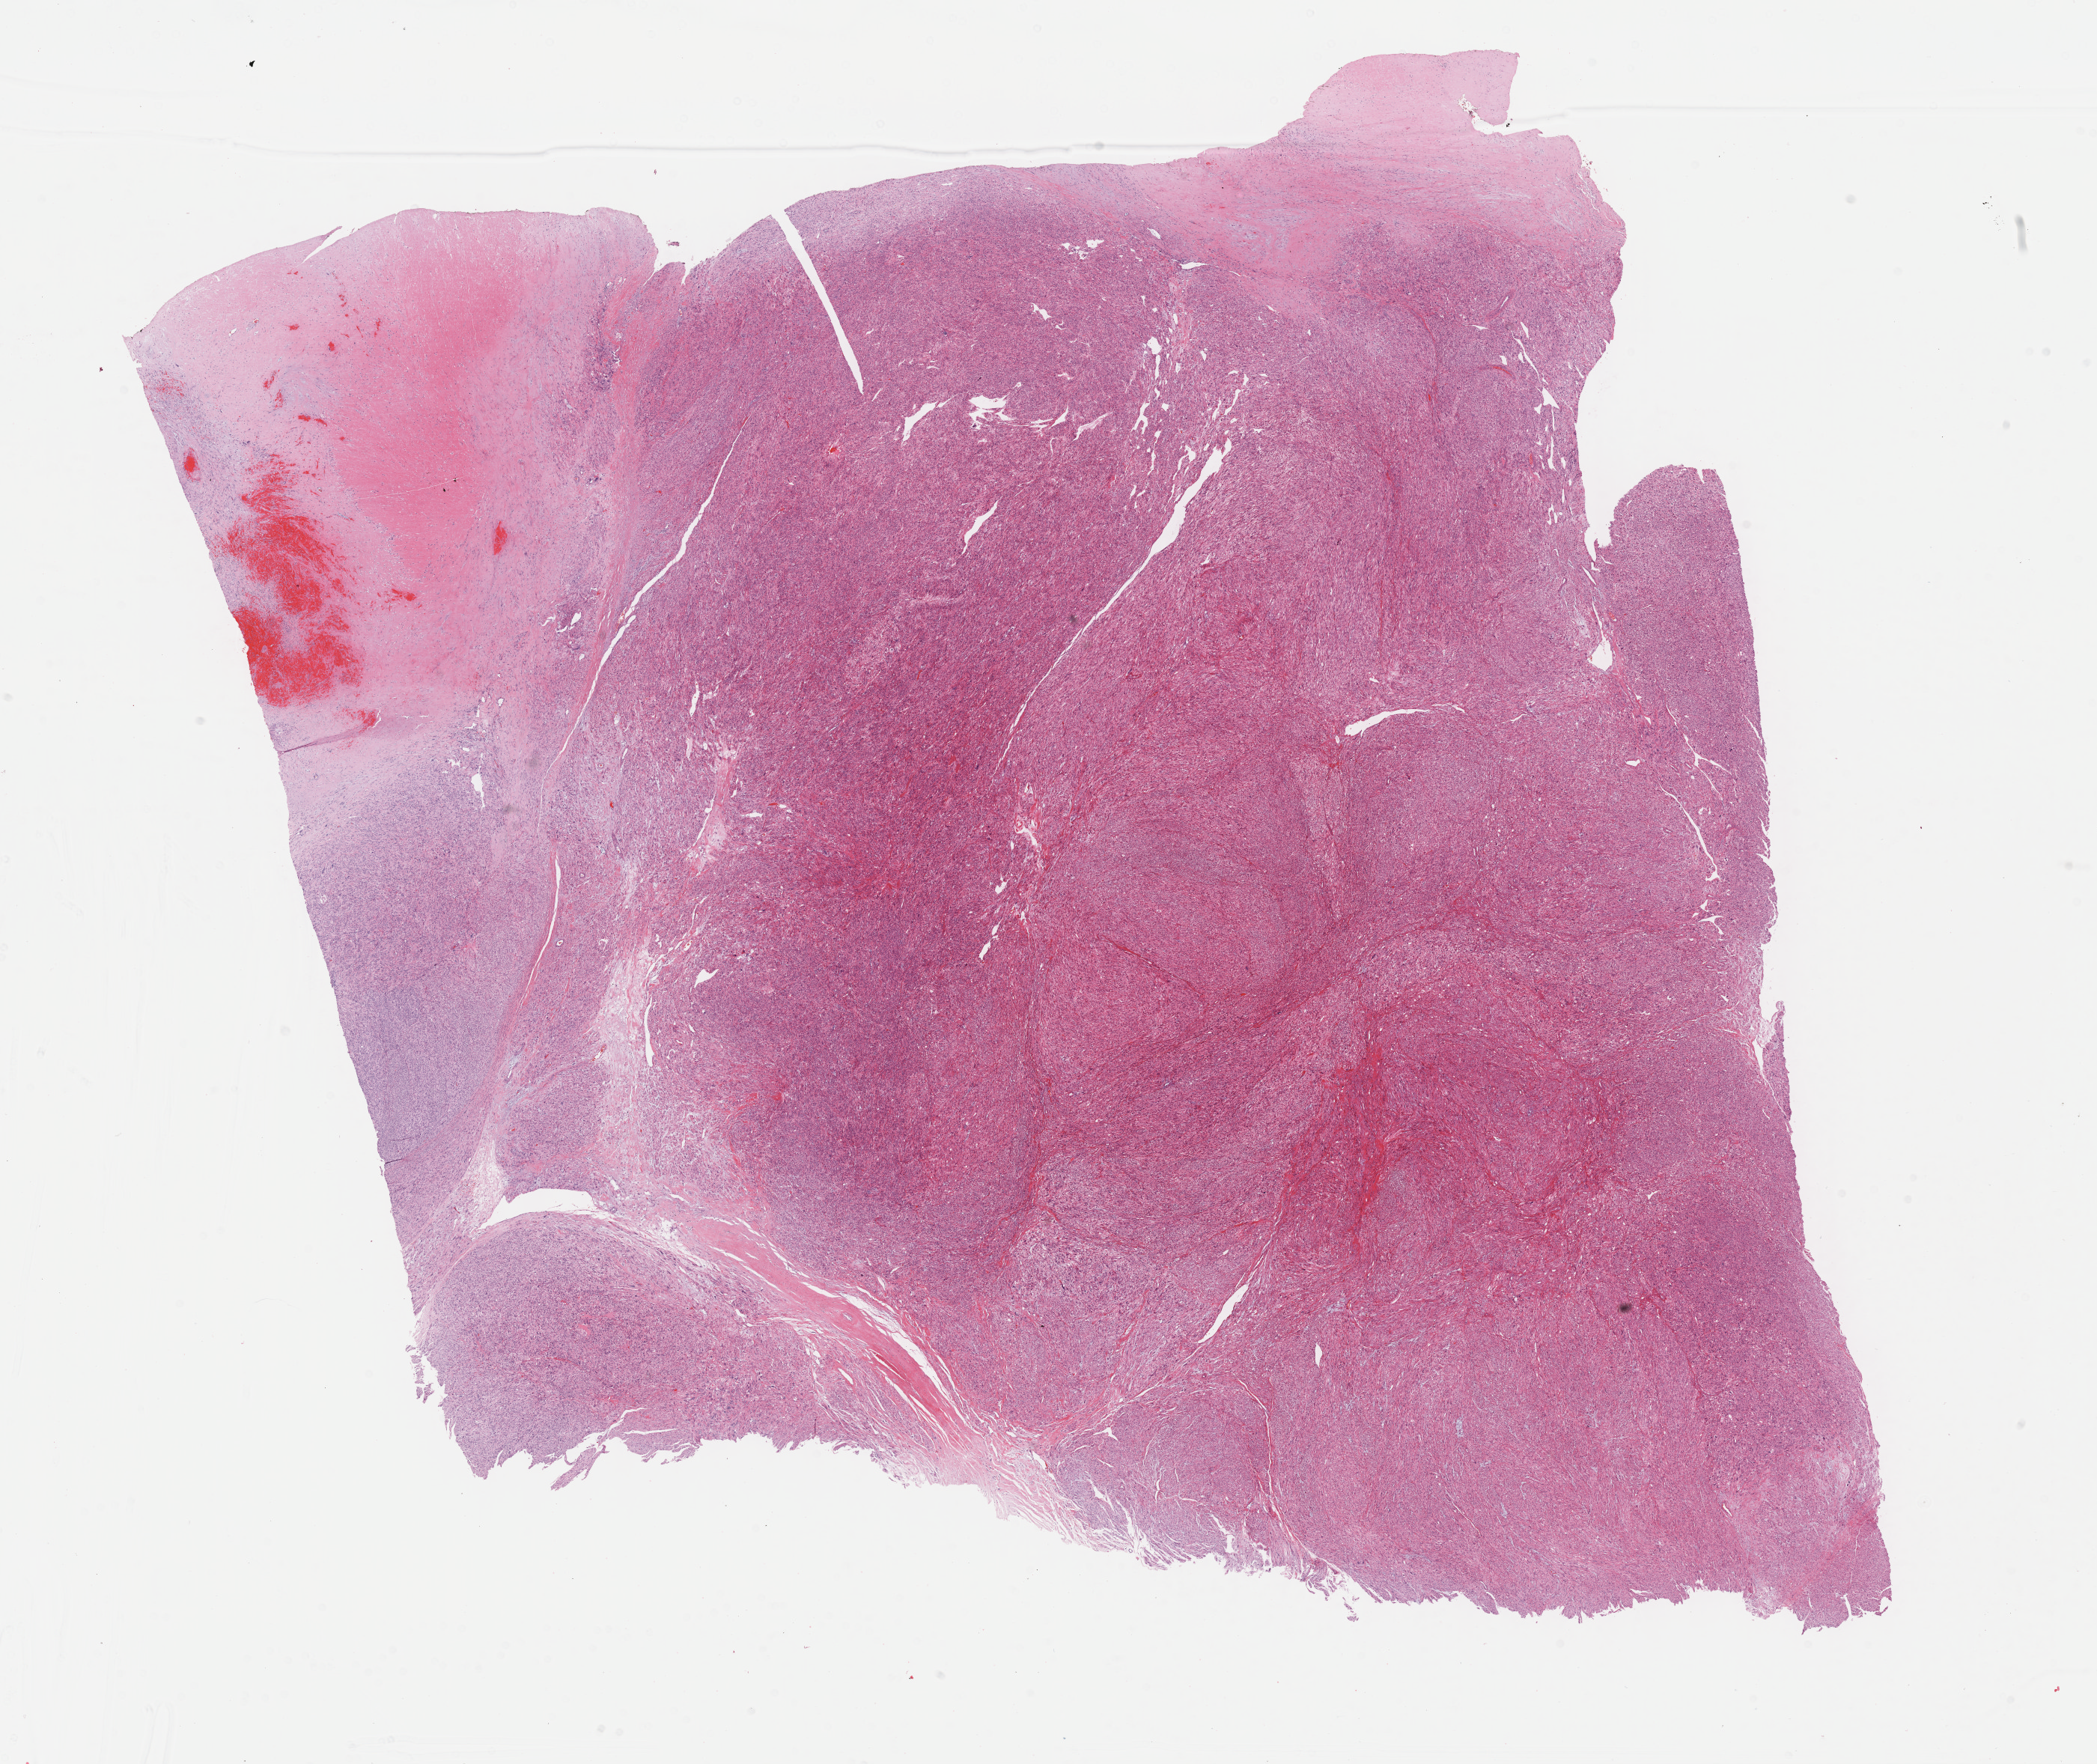
Digitized H&E tissue section (whole slide) — low-resolution overview of the scanned area, about 22.7 x 19.1 mm (slide scanned at 40x); formalin-fixed paraffin-embedded (FFPE) diagnostic section; sample: primary tumour, connective, subcutaneous and other soft tissues. Female, age 56 years at initial diagnosis.
Pathologic diagnosis: Leiomyosarcoma, NOS.